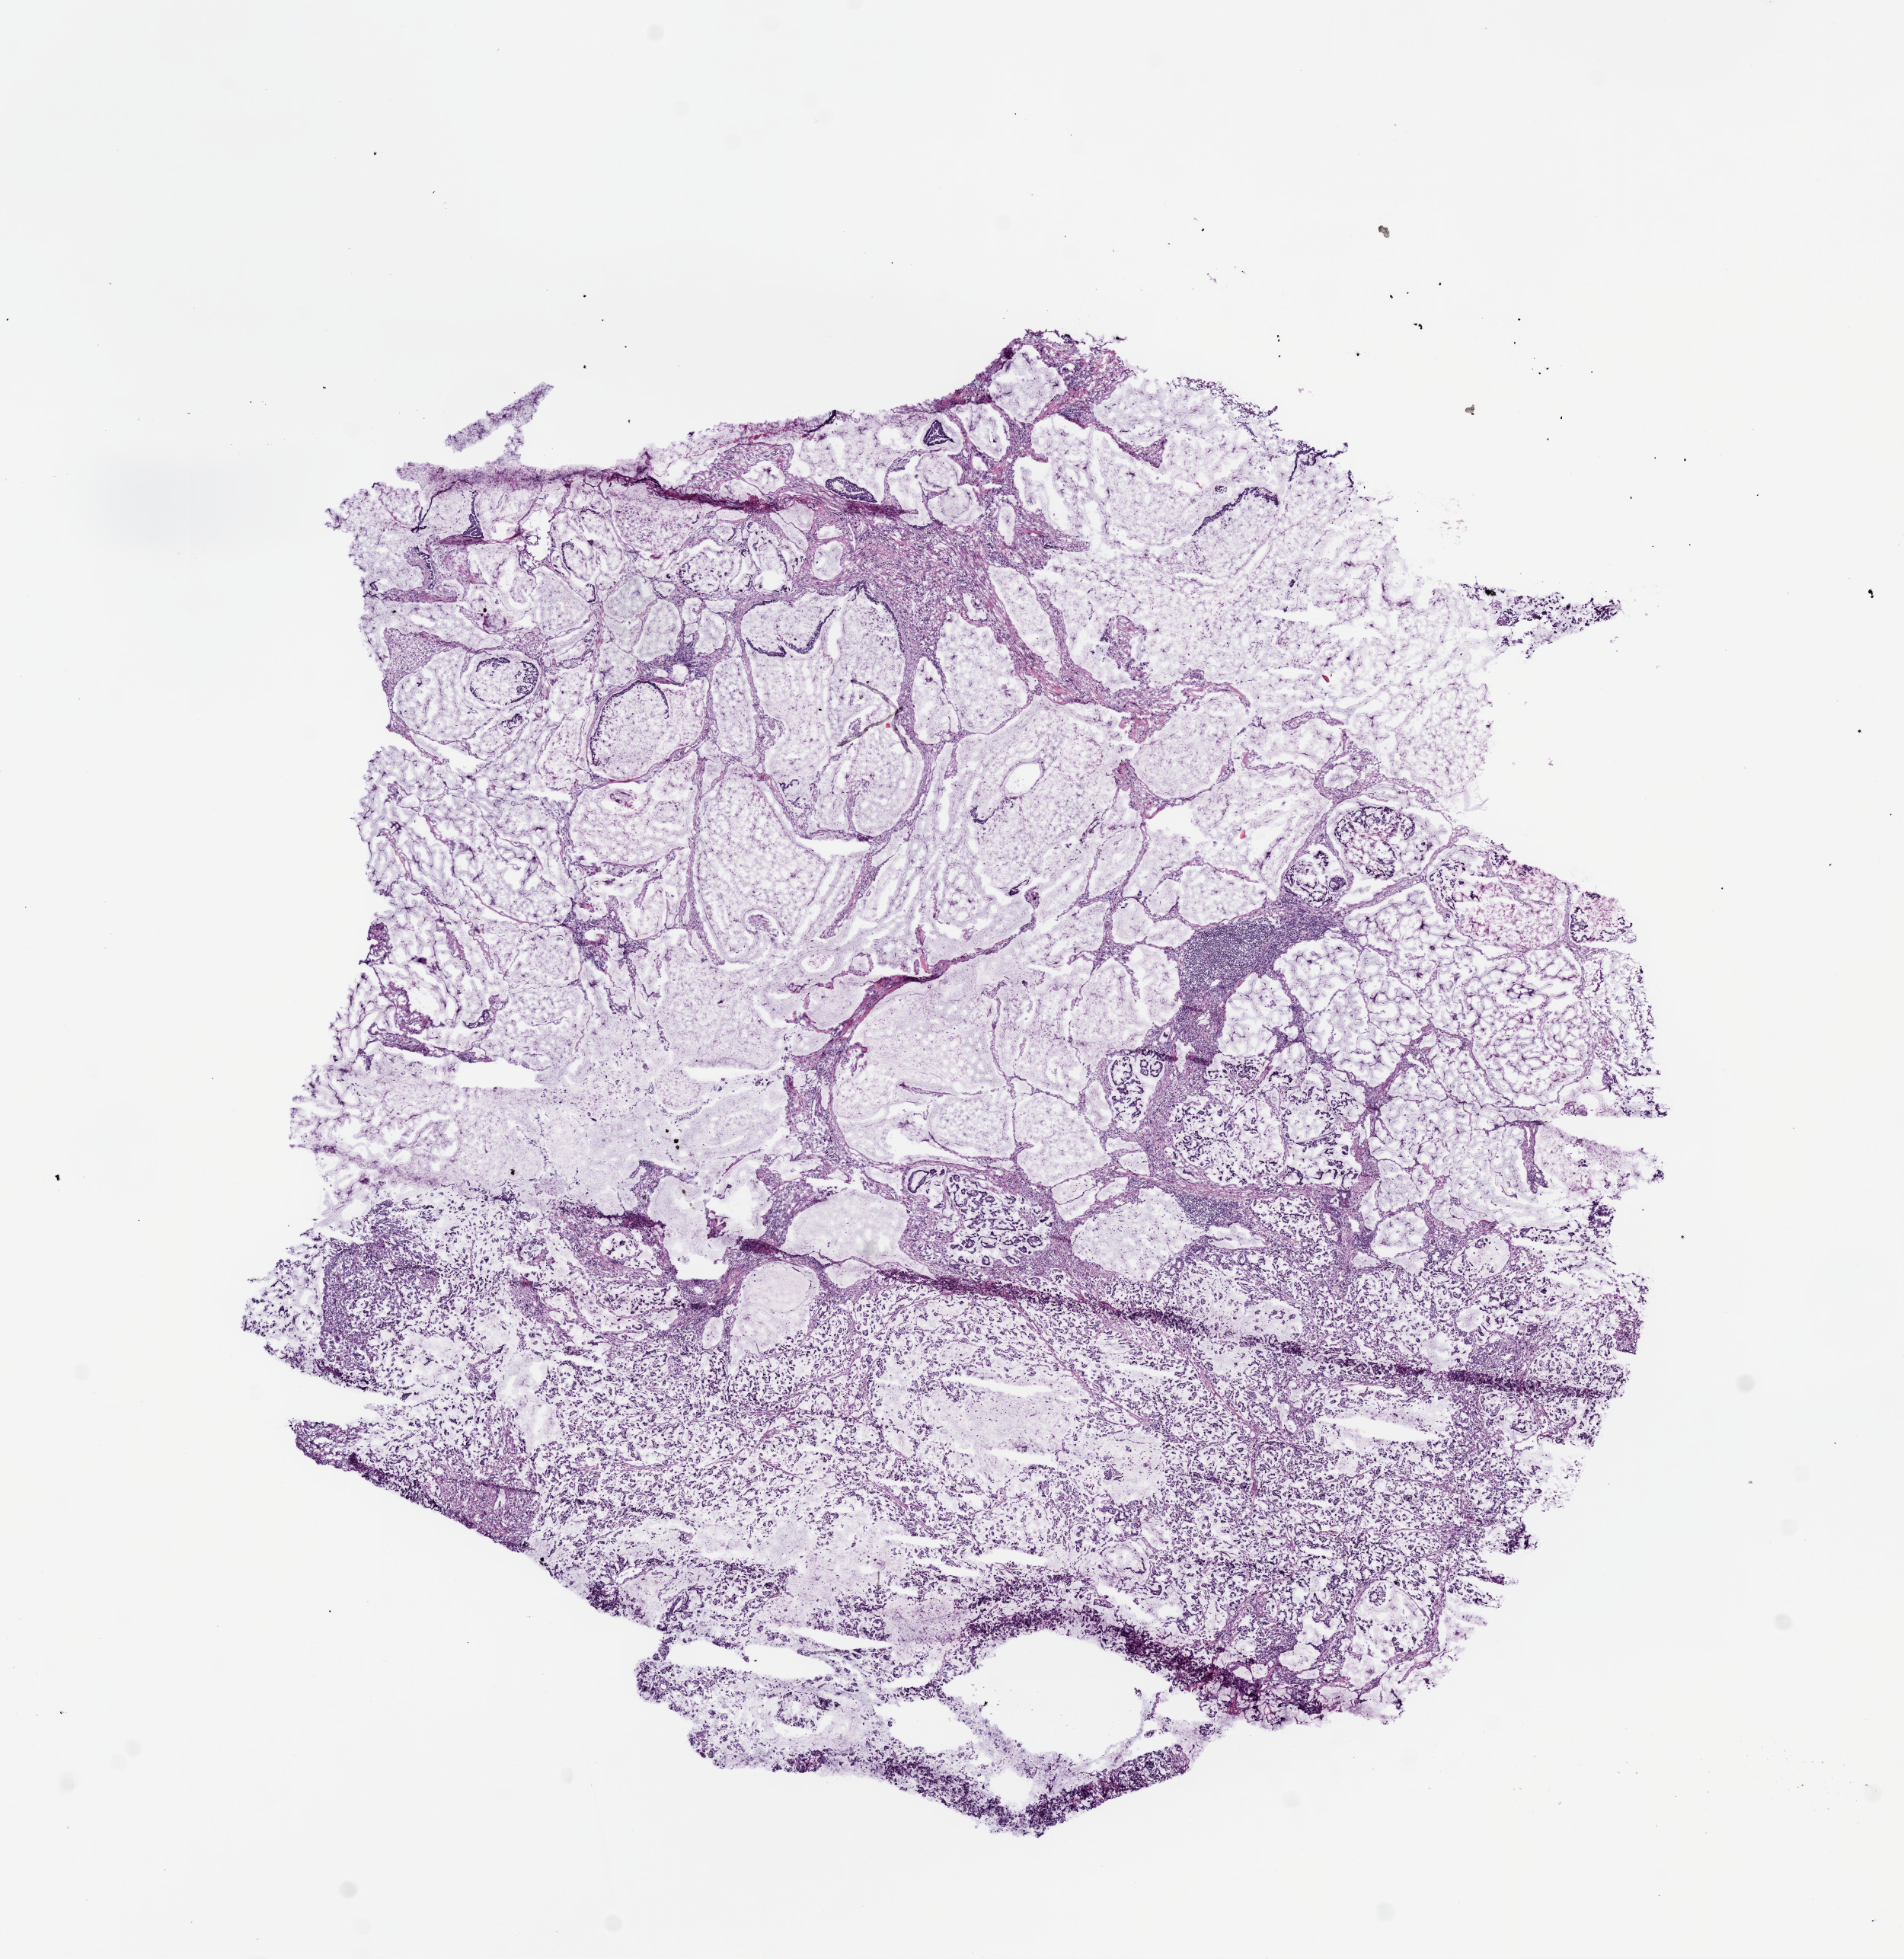
Whole-slide histology image, H&E-stained — whole scanned area (about 10.0 x 10.3 mm, from a 20x scan) shown as a low-resolution overview. Frozen section. Stomach, primary tumour sample. Male, age 72 years at initial diagnosis. Histologic grade: G3 (poorly differentiated). Composition of this section per pathologist review: tumour cells 95%, tumour nuclei 80%, normal cells 0%, stromal cells 5%, necrosis 0%.
AJCC pathologic stage: II. Histologic diagnosis: Mucinous adenocarcinoma. Lymph nodes positive (case pathology): 2 of 17 examined.